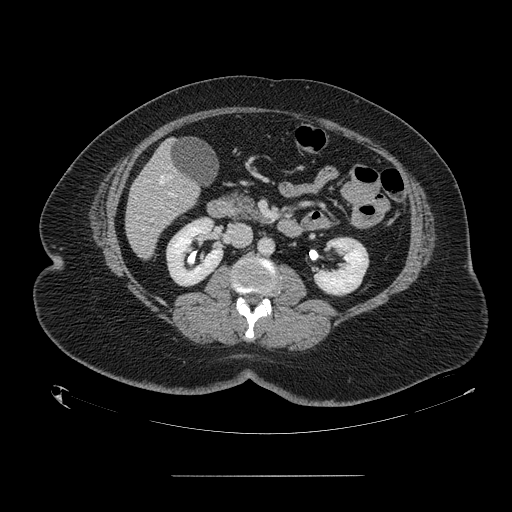
Contrast-enhanced abdominal CT, one axial slice; slice 55 of 164 in the series (ordered by position); 120 kVp; intravenous contrast given; soft-tissue window (W 400 / L 40 HU); 2.5 mm slice thickness; 512 × 512 image matrix. Female patient, age 52 years. From the clinical record (not read from this slice): diagnosis: colorectal cancer liver metastases, imaged before liver resection; multiple liver metastases: yes; largest metastasis: 3.5 cm; chemotherapy before resection: no.
Annotated regions visible in this slice (outlined manually by an expert reader):
- hepatic veins: box from (x=137, y=175) to (x=172, y=230) px
- liver: (x=126, y=144)–(x=200, y=258)
- portal vein (with intrahepatic branches): (x=169, y=192)–(x=172, y=195)